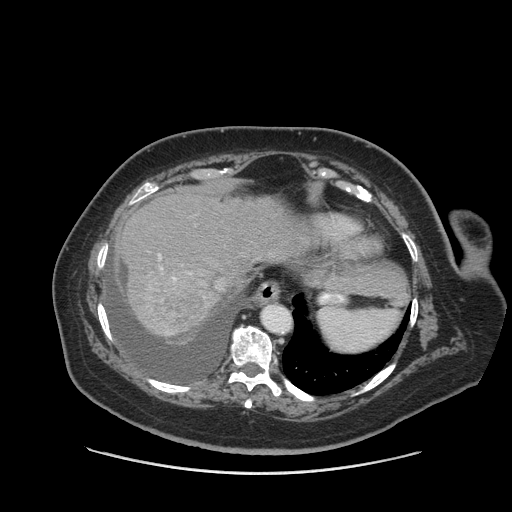
Contrast-enhanced abdominal CT (liver protocol), one axial slice. Position 70 of 91 along the scan axis. Soft-tissue window (W 400 / L 40 HU). 512 × 512 image matrix, field of view 420 × 420 mm. From the clinical record (not read from this slice): diagnosis: hepatocellular carcinoma (patient treated with transarterial chemoembolisation; whether this scan precedes or follows treatment is not stated here); TNM stage (as recorded): Stage-I; Child-Pugh class: A; tumour nodularity: uninodular.
Structures marked on this image (semi-automatic segmentation, software-assisted and operator-edited):
- abdominal aorta: bounding box <263,306,290,332> (left, top, right, bottom; pixels)
- liver parenchyma outside the tumour (the mass and vessels are separate outlines, so this box may not span the whole liver): <114,186,320,336>
- mass: <146,293,207,332>
- liver vessels: <158,254,177,281>